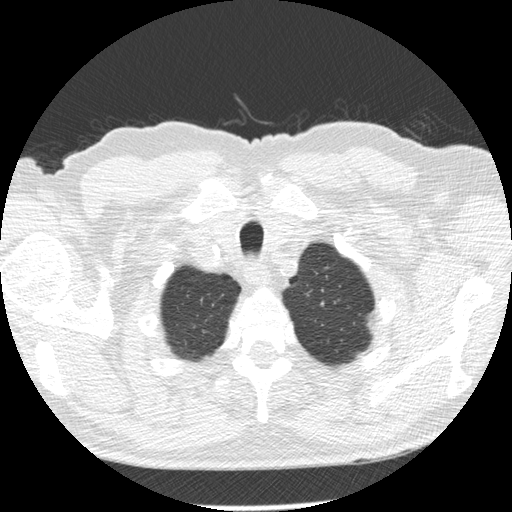
Axial slice from a low-dose chest CT screening exam. Second annual screen. Lung window (W 1500 / L -600 HU). Standard (soft-tissue) reconstruction kernel (STANDARD). Slice 25 of 276 in the series. Male, age 73 years at enrolment.
- Expert-annotated lung lesion, bounding box (x1, y1, x2, y2) in pixels: (352, 303, 393, 347).
- Screening reader's record for this exam: no non-calcified nodule ≥4 mm recorded.